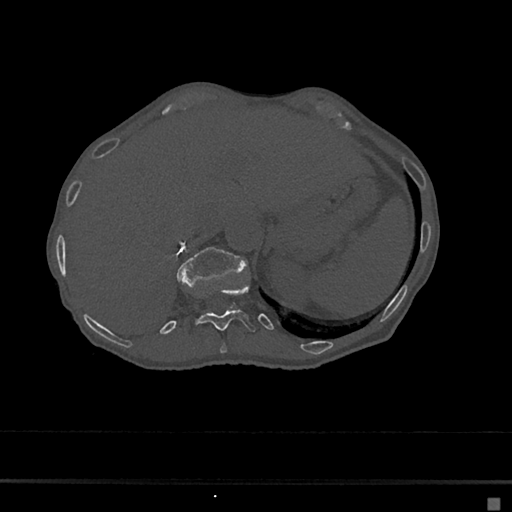
CT including the spine, one axial slice. Position 165 of 797 along the scan axis. Reconstruction kernel Br40s/3. Bone window (W 1800 / L 400 HU). 0.5 mm slice thickness. 512 × 512 image matrix, field of view 360 × 360 mm. Patient: female, 68 years. Case-level facts recorded for this patient, not image findings: primary cancer: renal.
Structures marked on this image (semi-automatic segmentation, software-assisted and operator-edited):
- T10 vertebra: bounding box (x1, y1, x2, y2) in pixels: (220, 343, 227, 354)
- T11 vertebra: (195, 283, 256, 332)
- T12 vertebra: (176, 247, 248, 286)